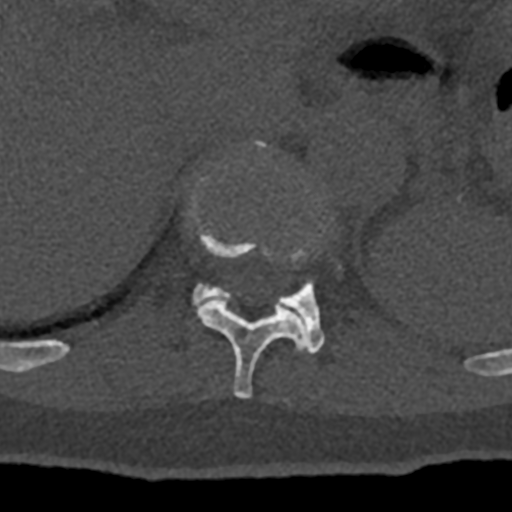
CT including the spine, one axial slice; position 527 of 797 along the scan axis; reconstruction kernel Br40s/3; bone window (W 1800 / L 400 HU); 512 × 512 image matrix, field of view 160 × 160 mm. Patient: male, 74 years. Case-level facts recorded for this patient, not image findings: primary cancer: renal.
Outlined on this slice (semi-automatically segmented with operator editing):
- T11 vertebra: box from (x=189, y=141) to (x=307, y=398) px
- T12 vertebra: (x=192, y=199)–(x=325, y=354)